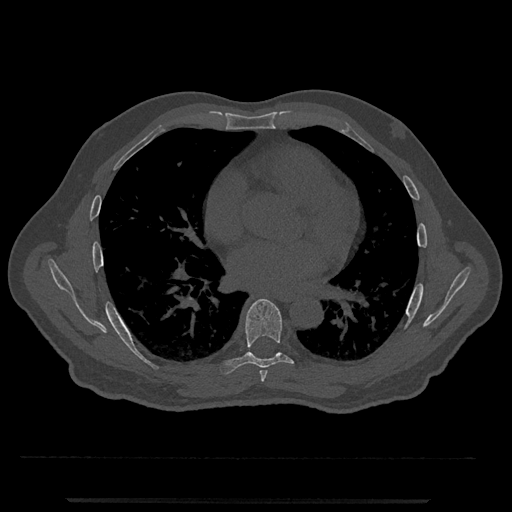
CT including the spine, one axial slice; position 687 of 797 along the scan axis; reconstruction kernel Br40s/3; bone window (W 1800 / L 400 HU); 0.5 mm slice thickness; 512 × 512 image matrix, field of view 419 × 419 mm. Patient: male, 63 years. From the clinical record (not read from this slice): primary cancer: prostate.
Annotated regions visible in this slice (semi-automatically segmented with operator editing):
- T6 vertebra: bounding box (x1, y1, x2, y2) in pixels: (259, 370, 267, 382)
- T7 vertebra: (219, 299, 294, 375)